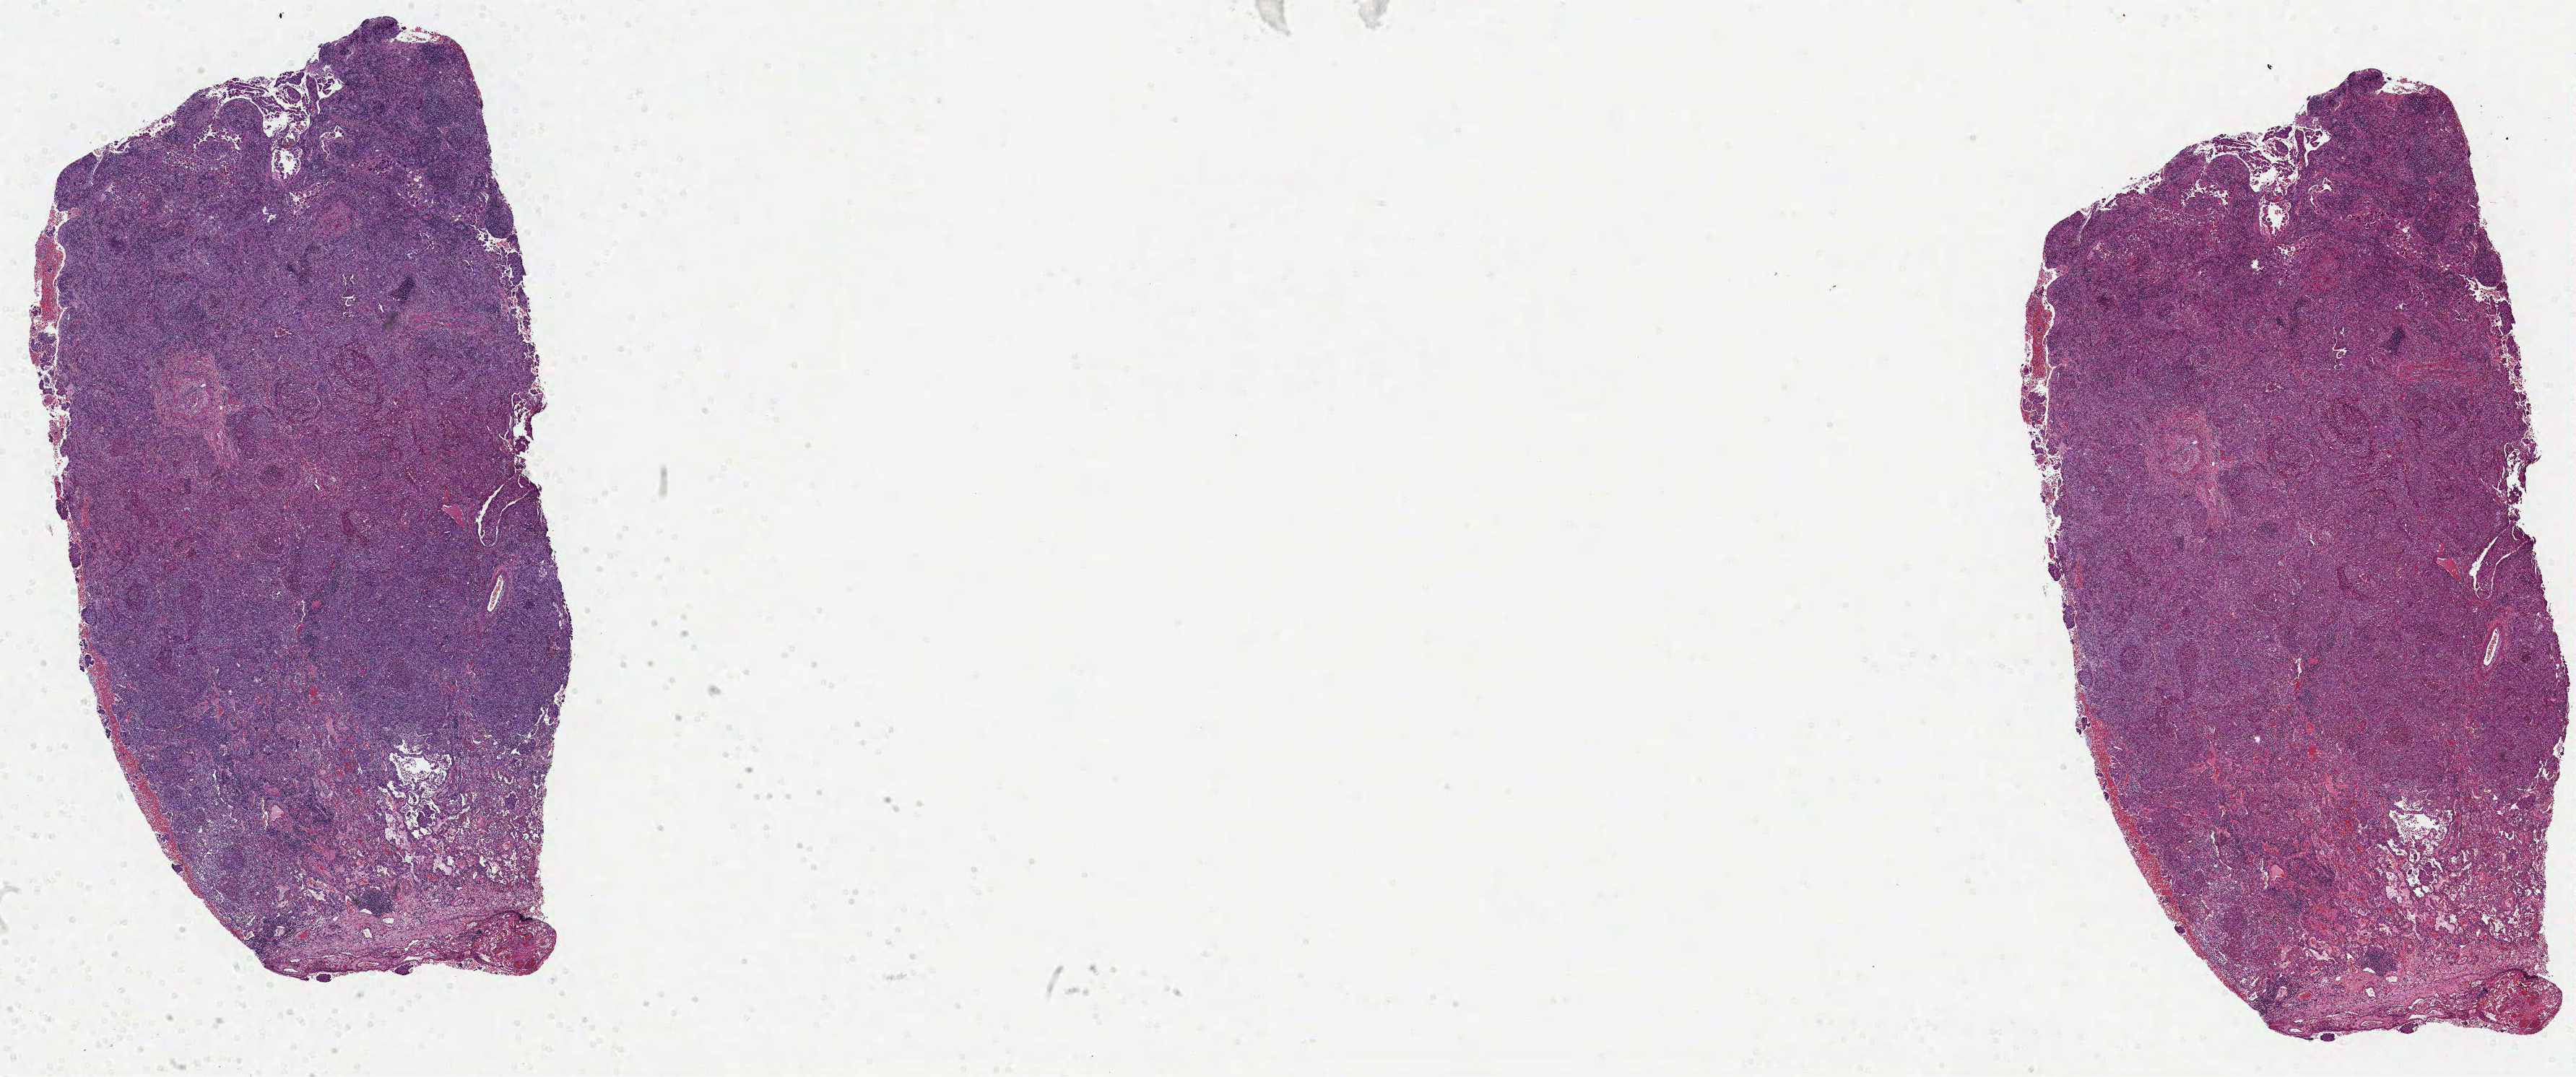
Hematoxylin and eosin (H&E) stained whole-slide image — low-resolution overview of the scanned area, about 28.8 x 12.0 mm; formalin-fixed paraffin-embedded (FFPE) diagnostic section; lung, primary tumour sample. Female patient; age at initial diagnosis 74 years.
AJCC pathologic stage: IIIA. Diagnosis: Adenocarcinoma, NOS (upper lobe, lung).